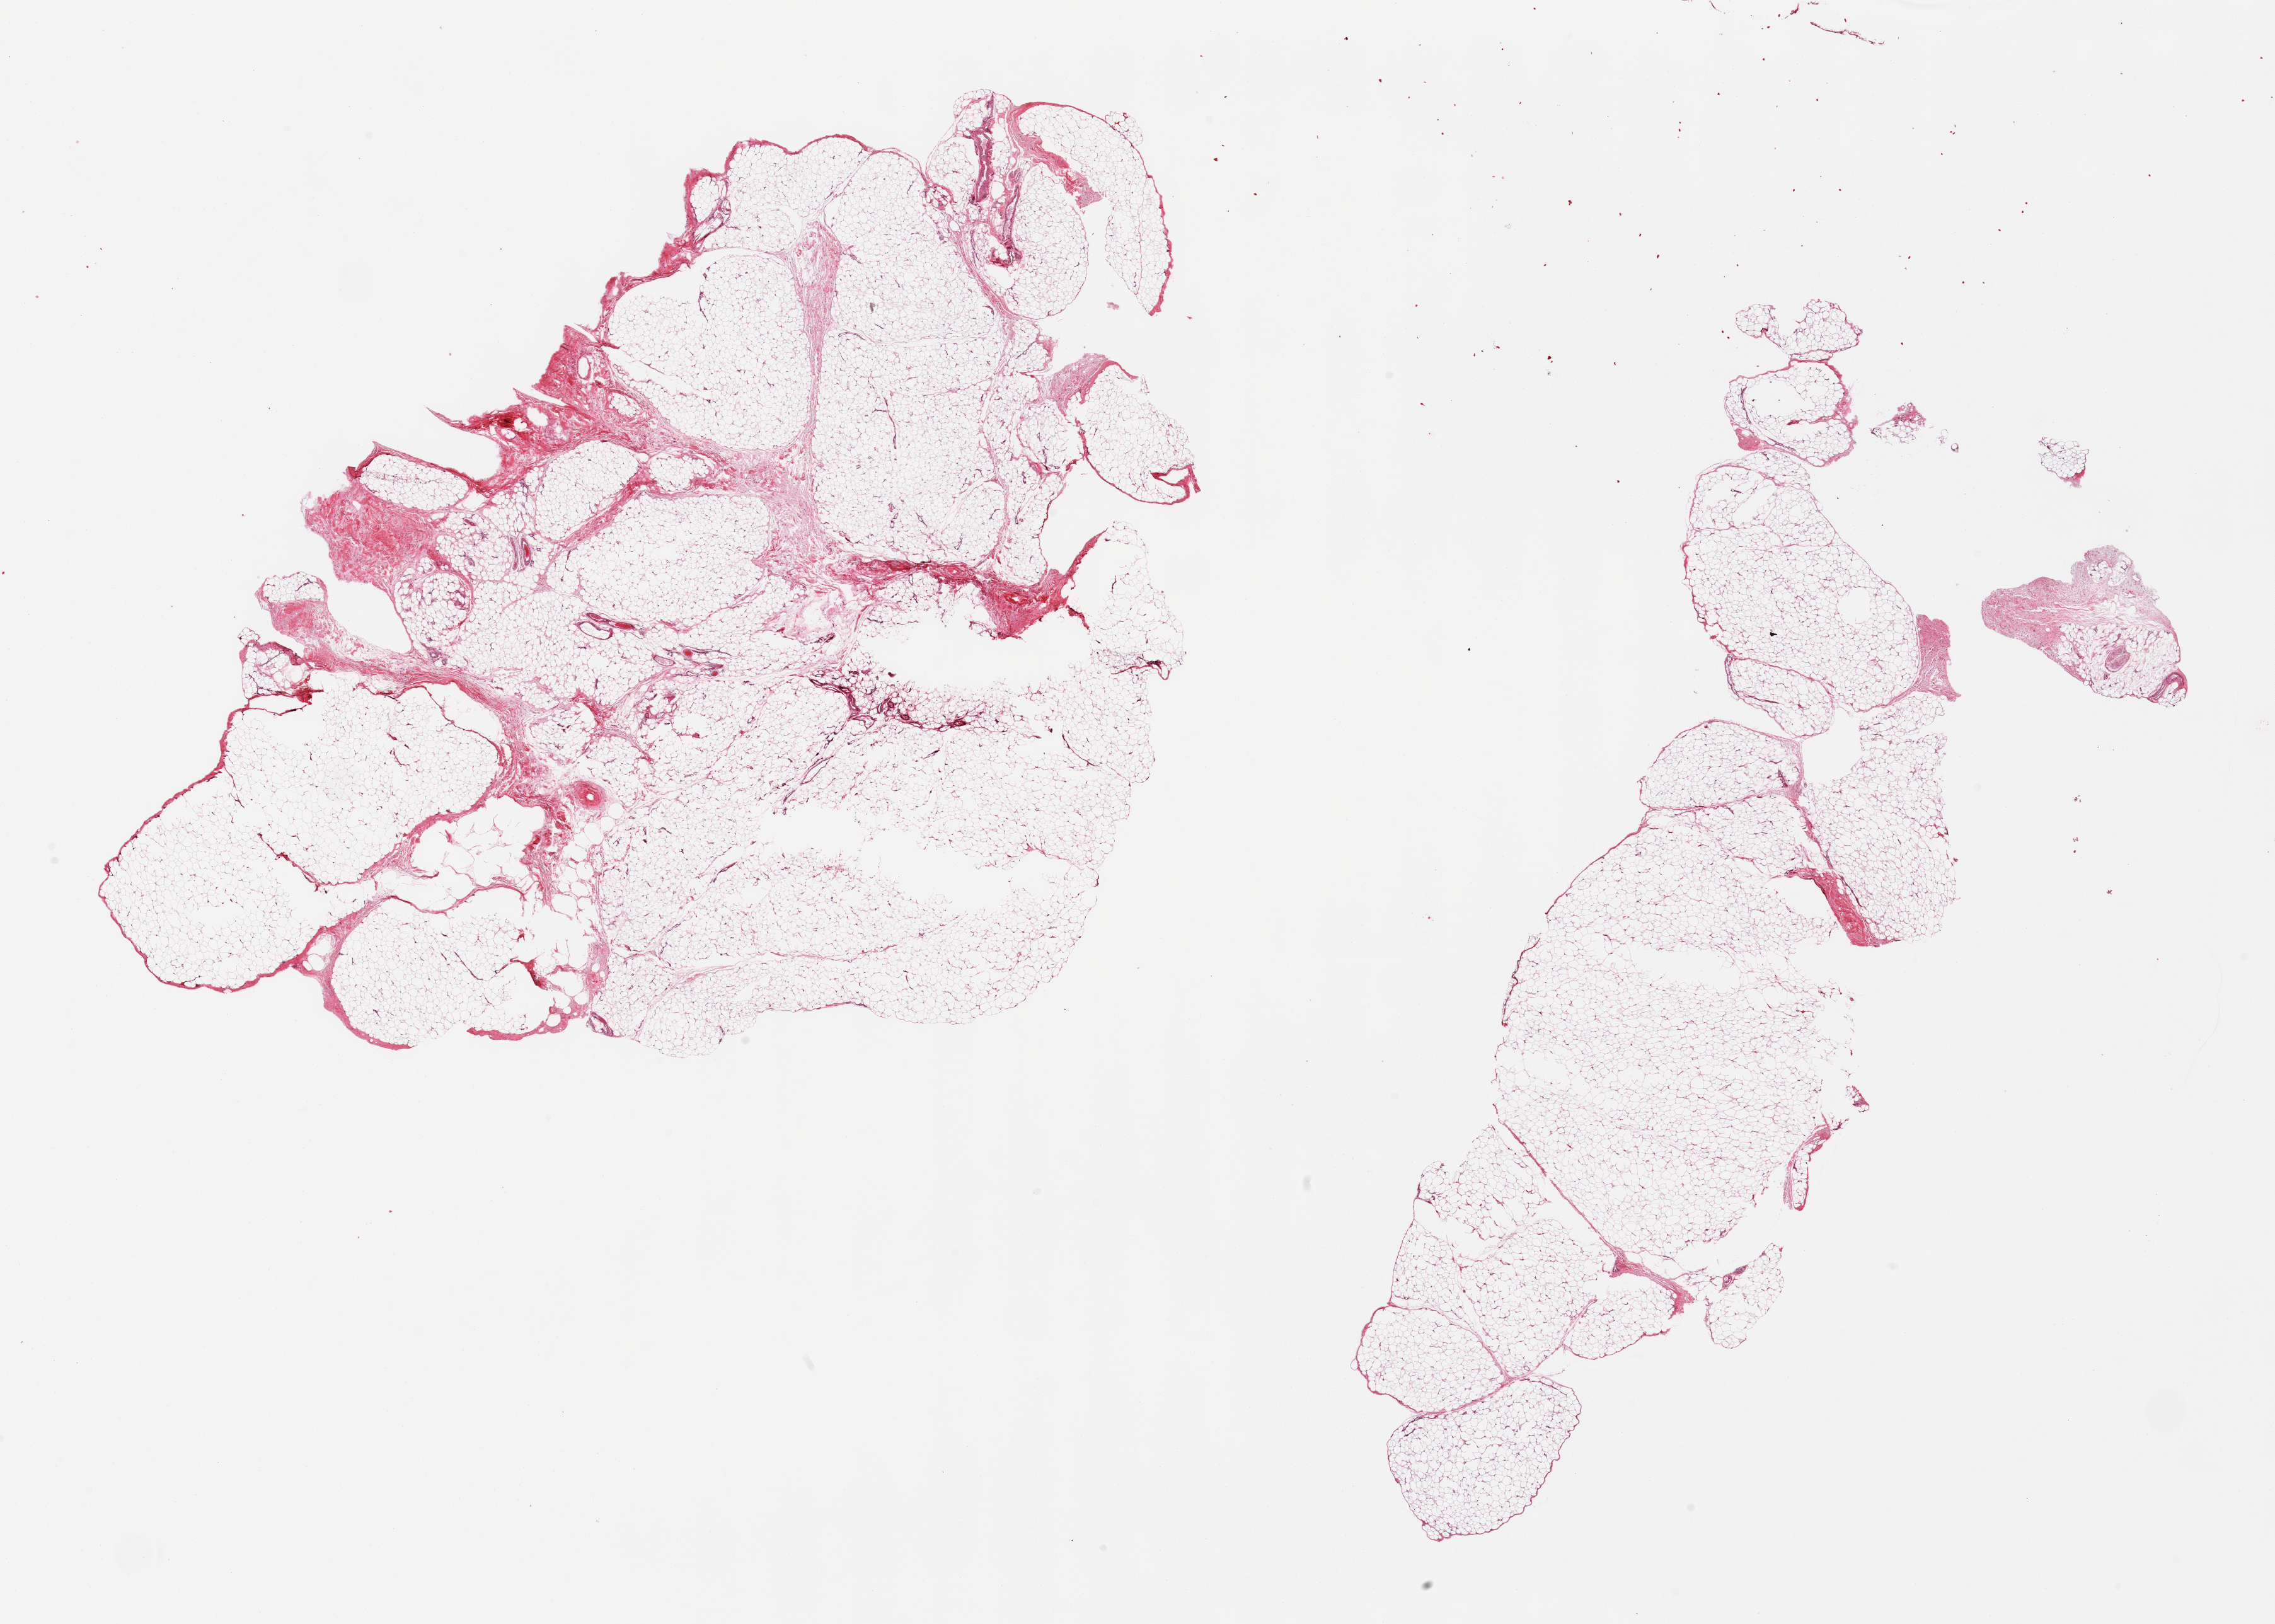
Hematoxylin and eosin (H&E) whole-slide image — whole scanned area (about 28.5 x 20.4 mm, from a 20x scan) shown as a low-resolution overview. PAXgene-fixed, paraffin-embedded tissue. Section of adipose tissue (target tissue). Donor tissue sample. Female donor.
Reviewer comment on this tissue sample: 2 pieces, ~10% interstitlal fascia.